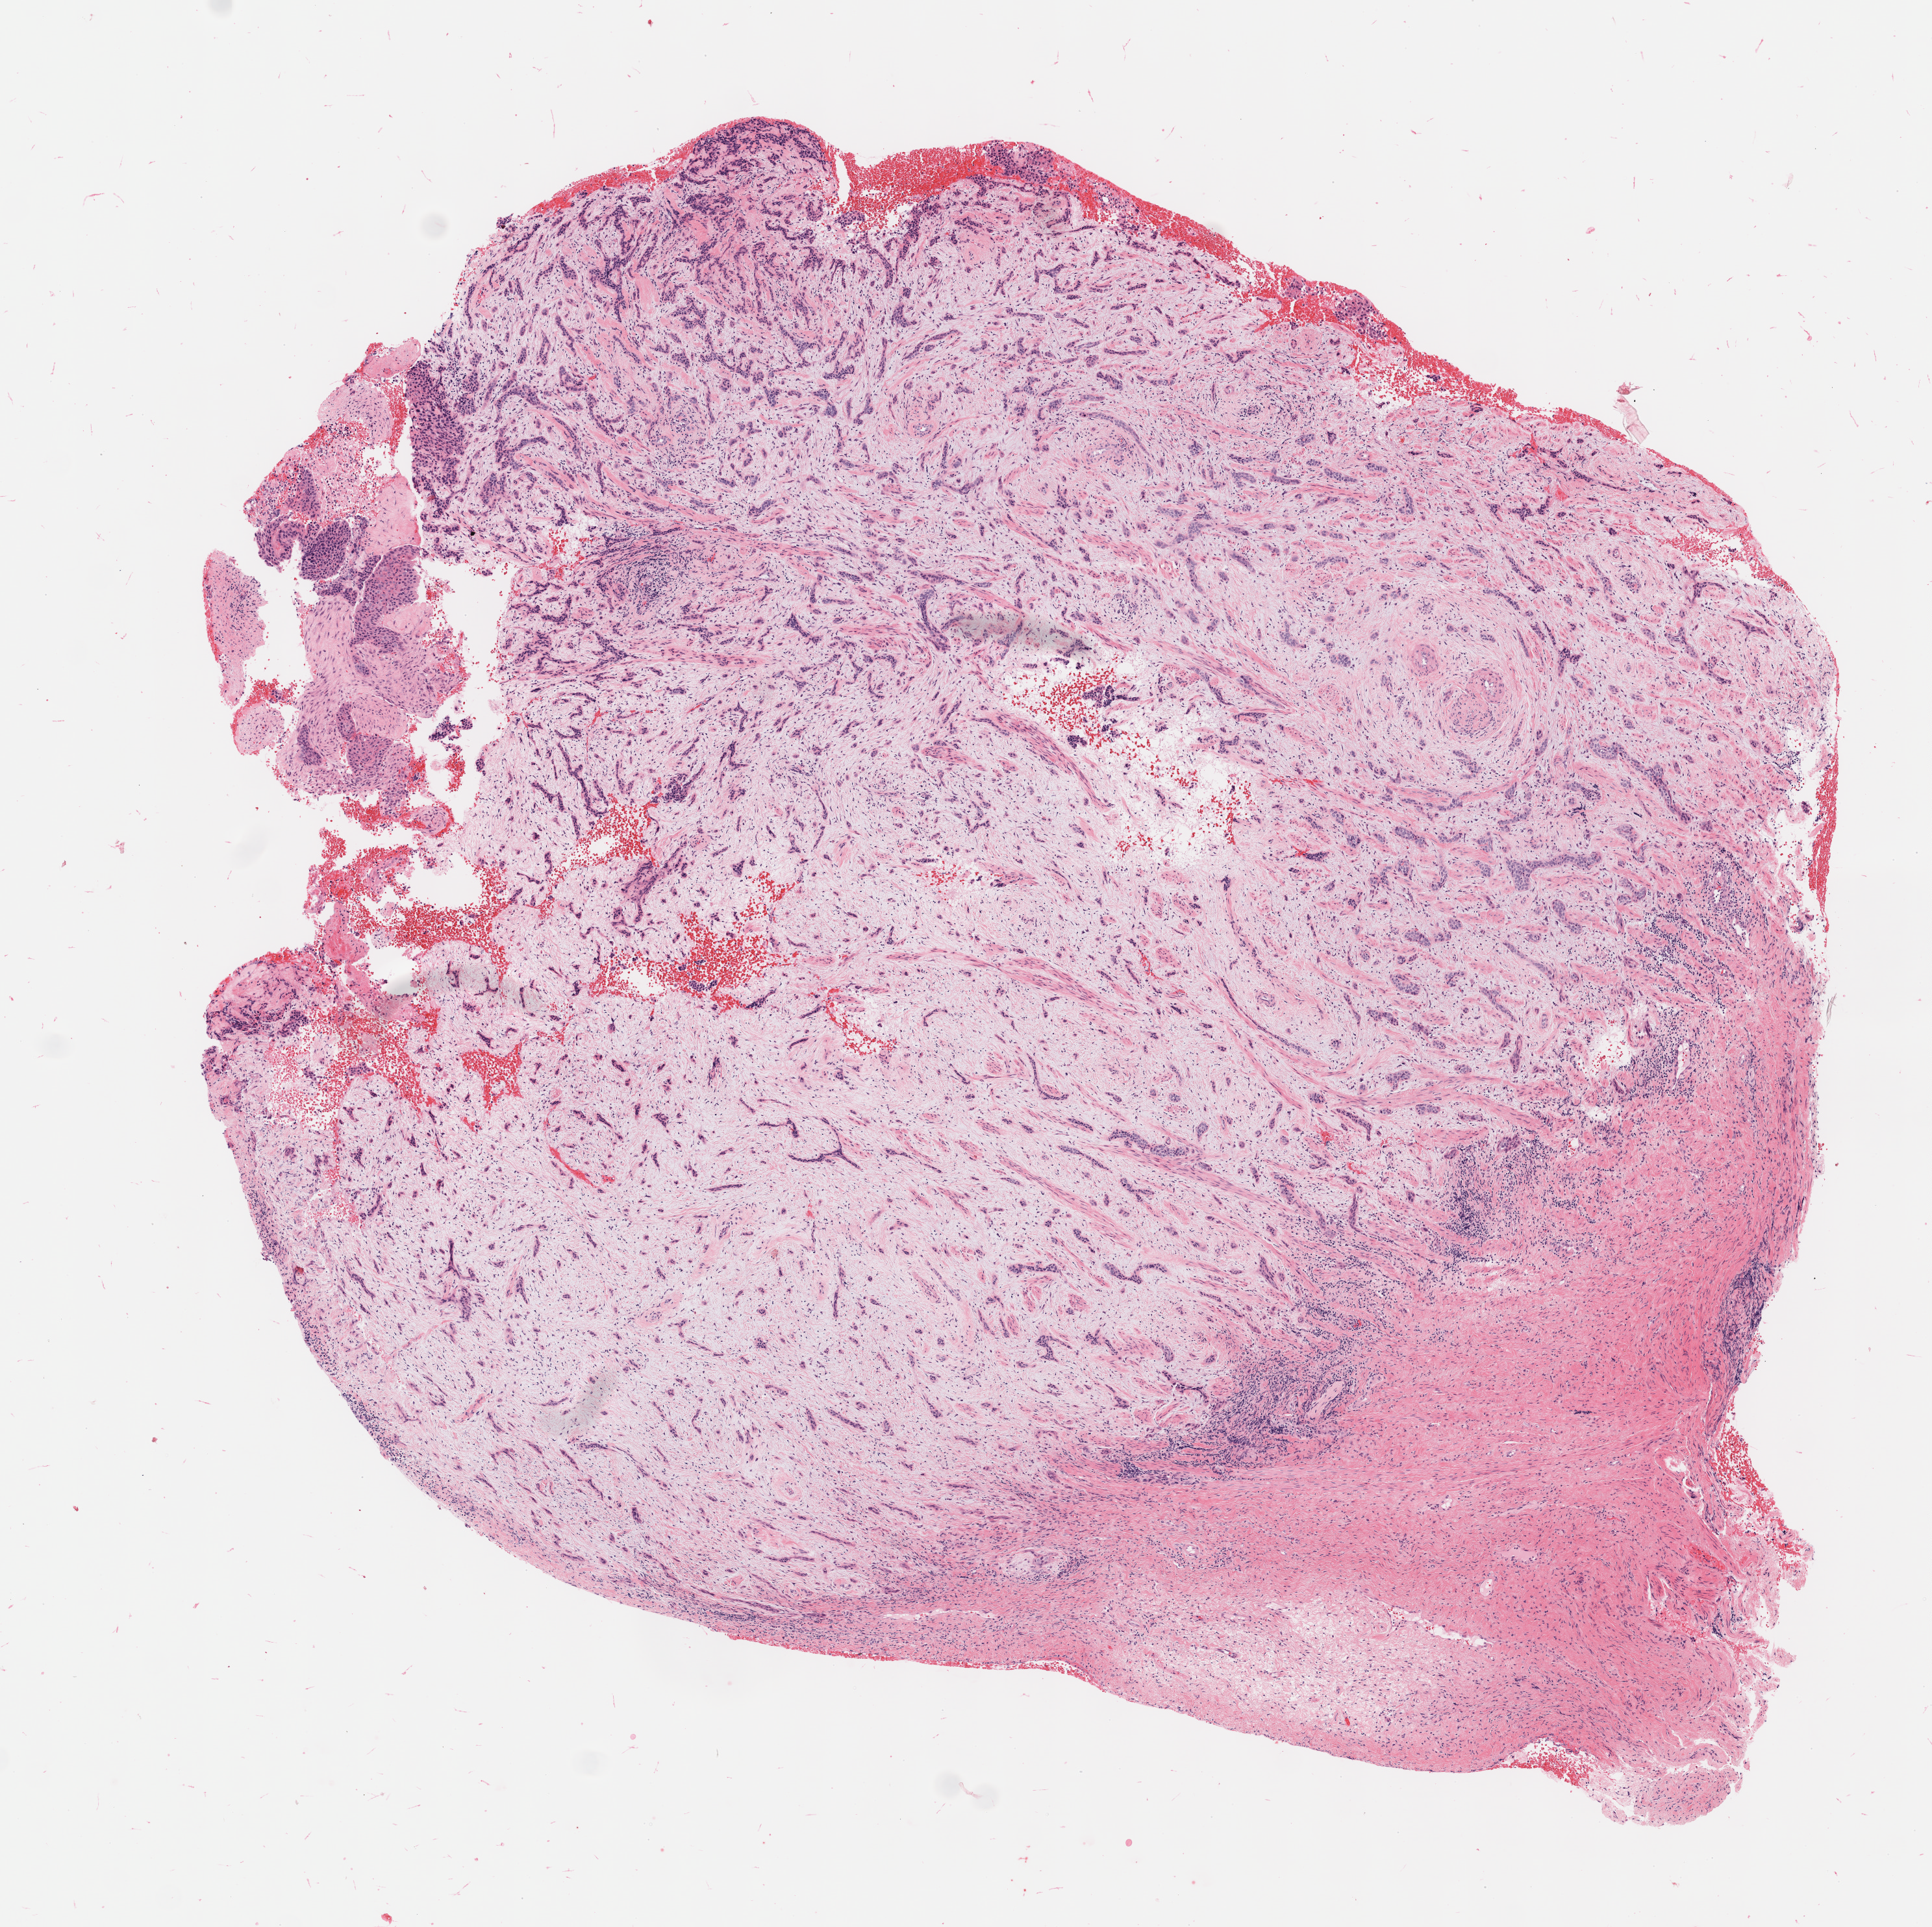
Whole-slide image, hematoxylin and eosin (H&E) stain, low-resolution overview of the scanned area, about 5.9 x 5.9 mm. Tumor tissue. Anatomic site: cervix. Female patient, 75 years old.
Histologic diagnosis: Squamous cell carcinoma, large cell, nonkeratinizing, NOS.